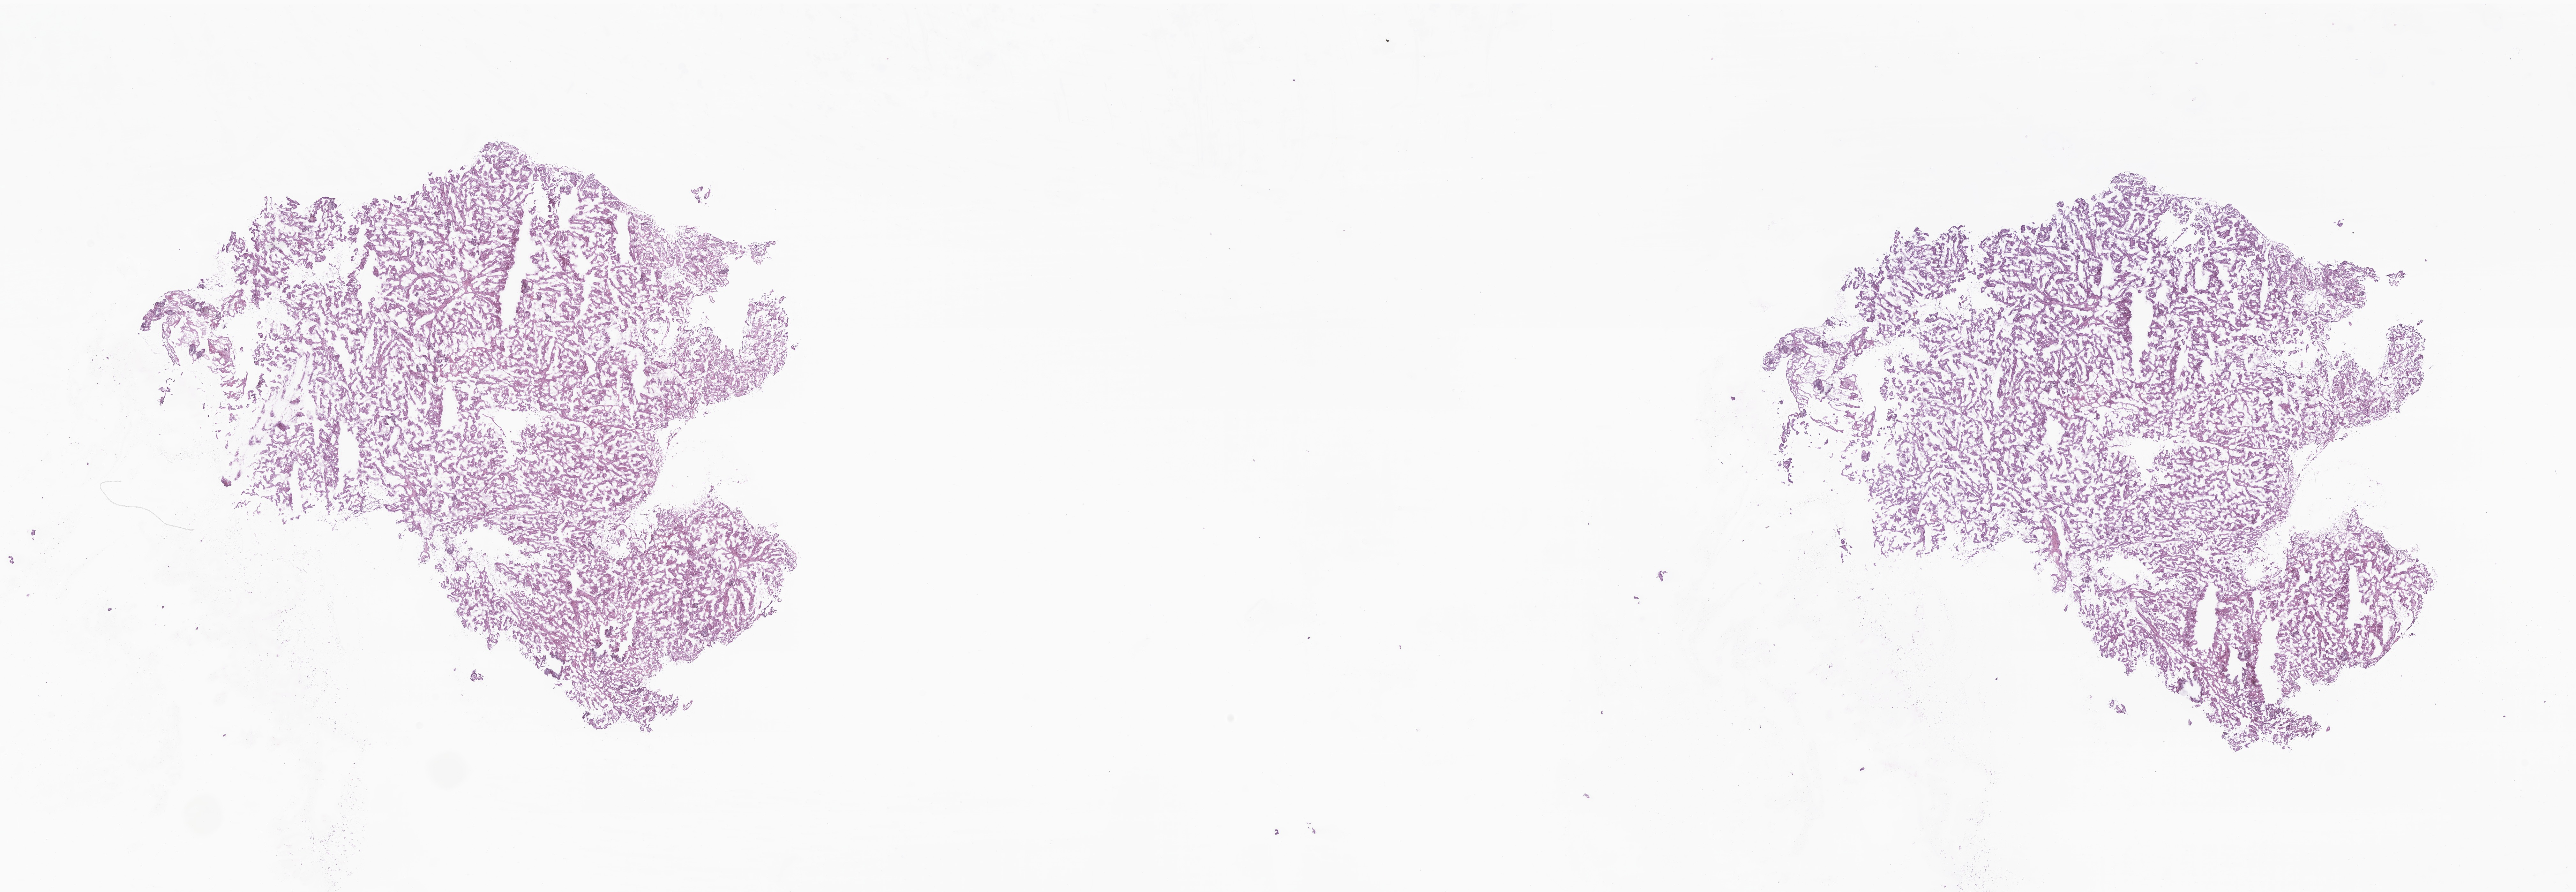
Digitized H&E-stained section of tumor tissue from the brain, low-resolution overview of the scanned area, about 34.0 x 11.8 mm. Frozen section (OCT-embedded). Patient: male, age 202 months (16 years 10 months).
Diagnosis (ICD-O-3 morphology term): Choroid plexus papilloma, NOS.